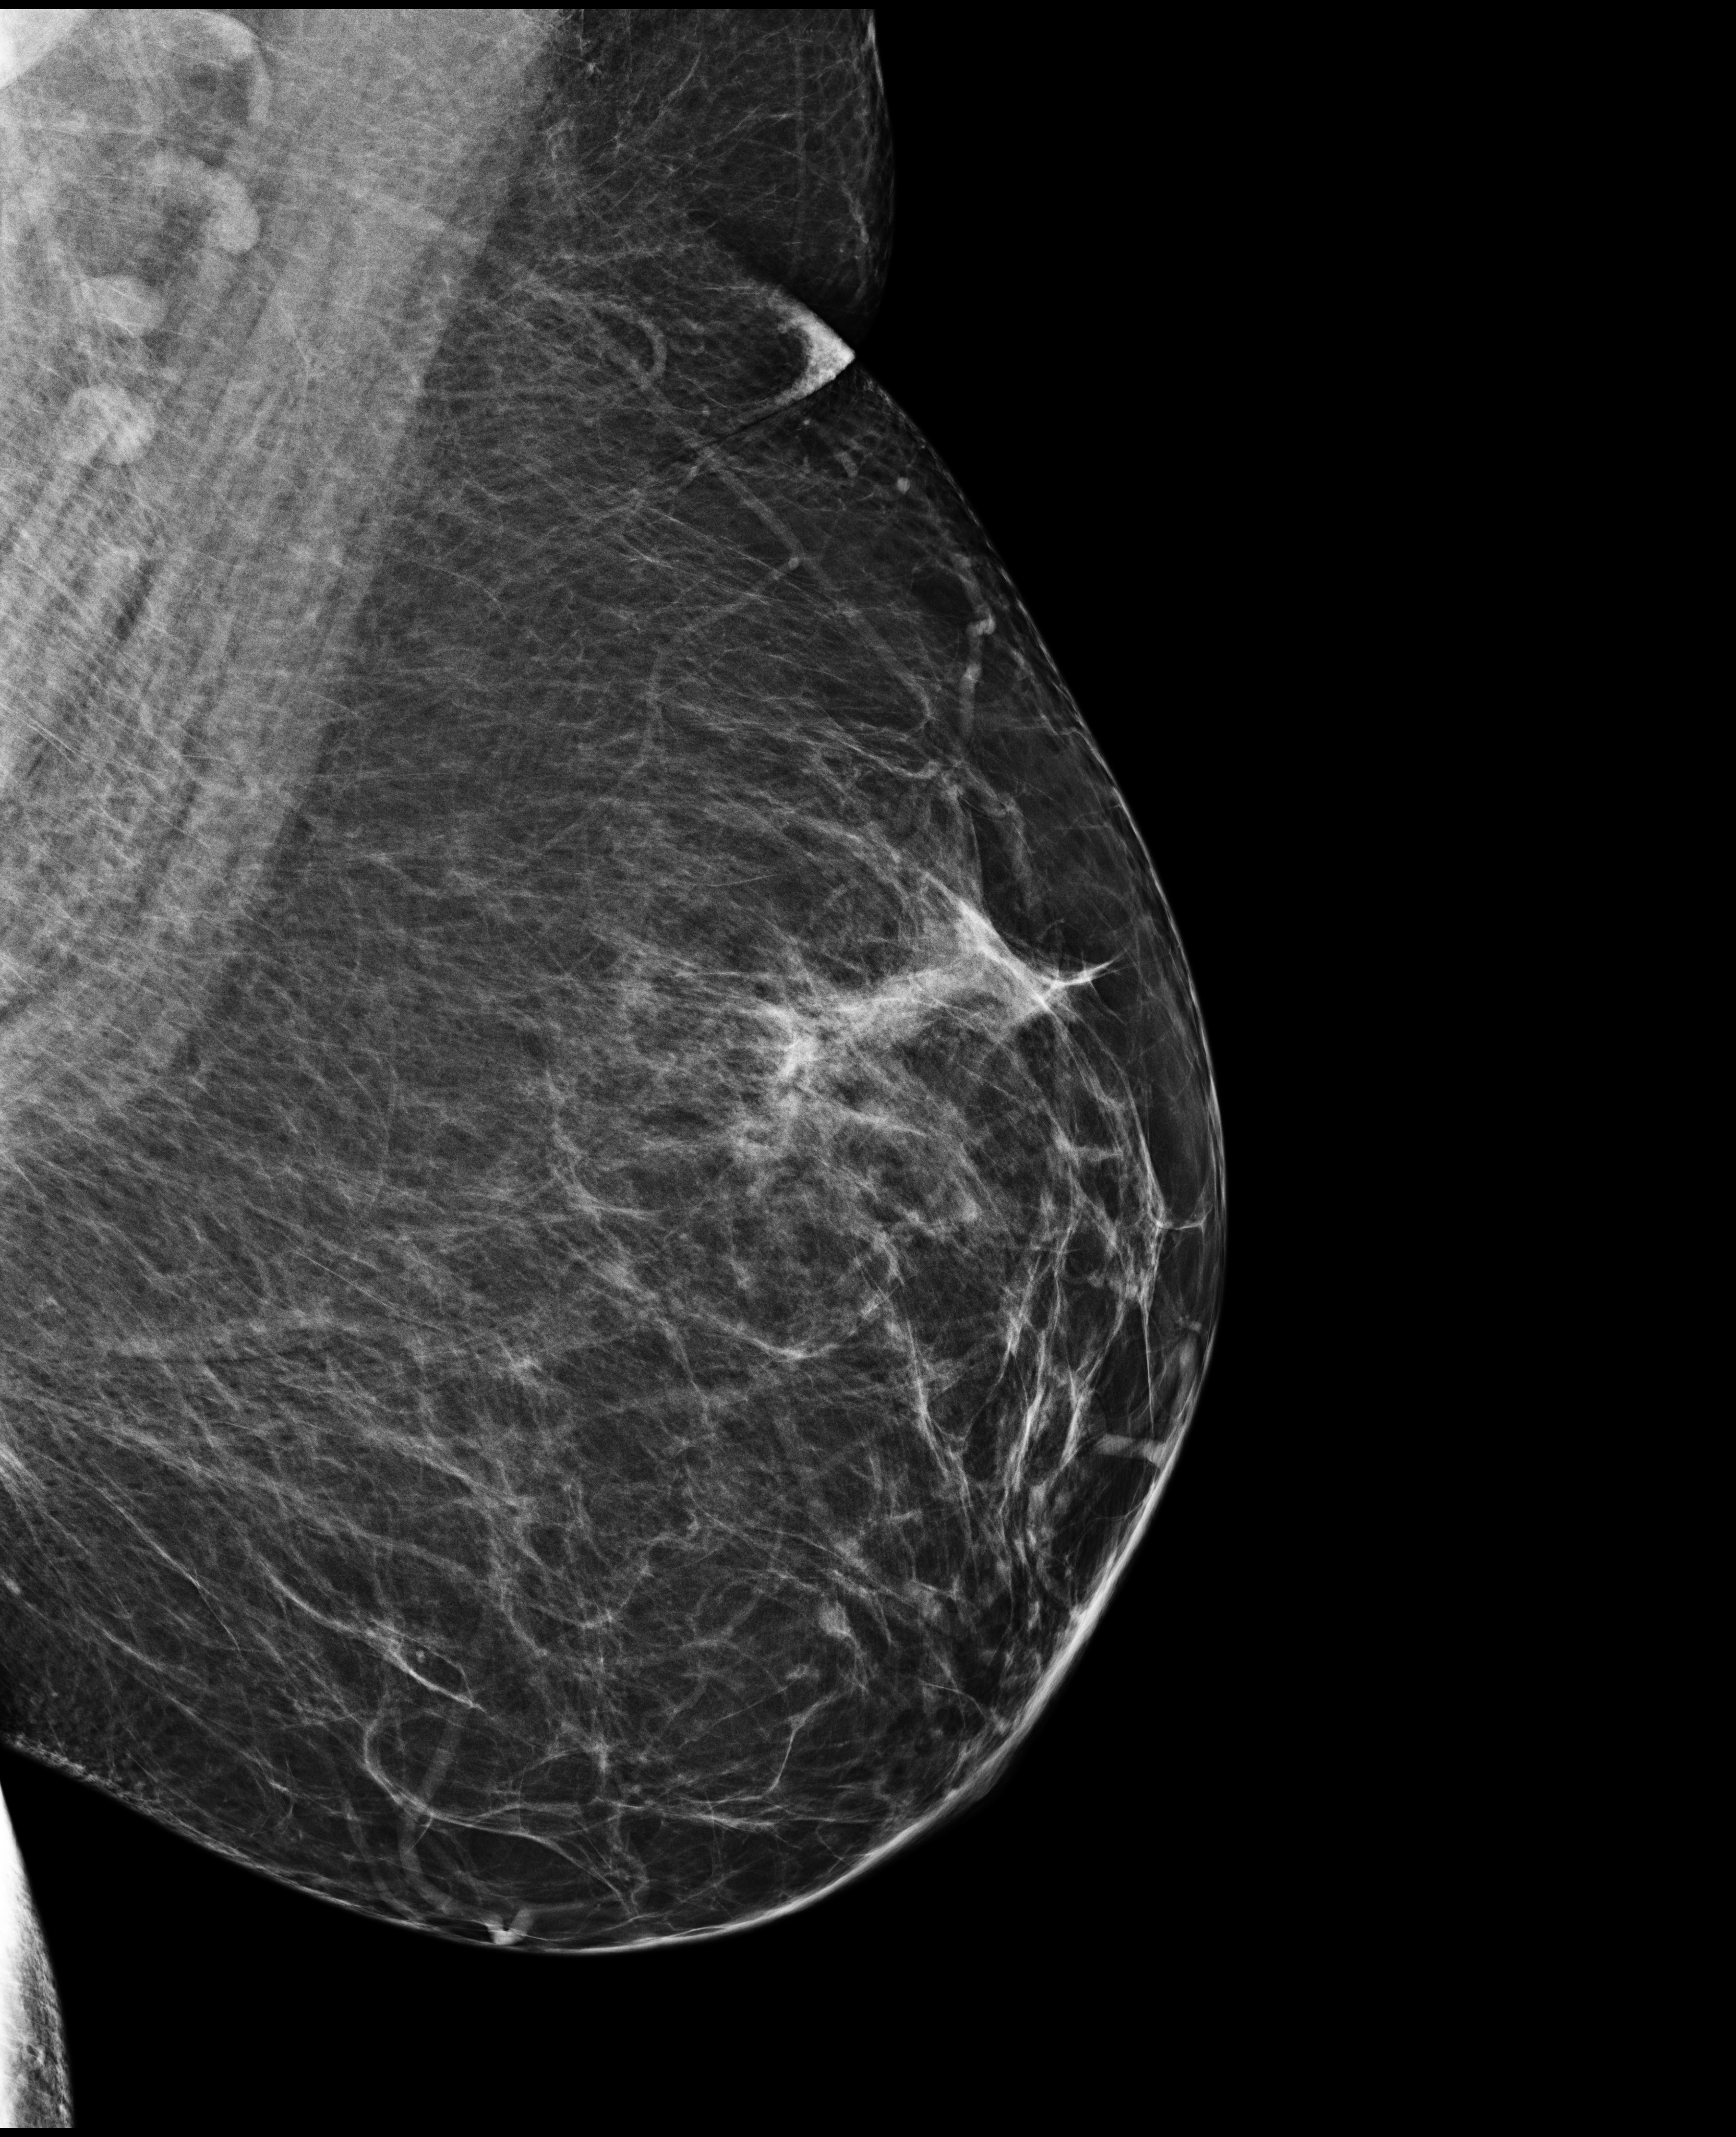
Full-field digital mammogram (FFDM), left breast, MLO view, screening examination, compressed breast thickness 88 mm. Patient aged 52 years (female).
BI-RADS breast density category at the screening exam (both breasts, scale 1–4): 2. Final BI-RADS category for the screening round (tomosynthesis exam, both breasts): category 2. Recall: no recall after this screen.